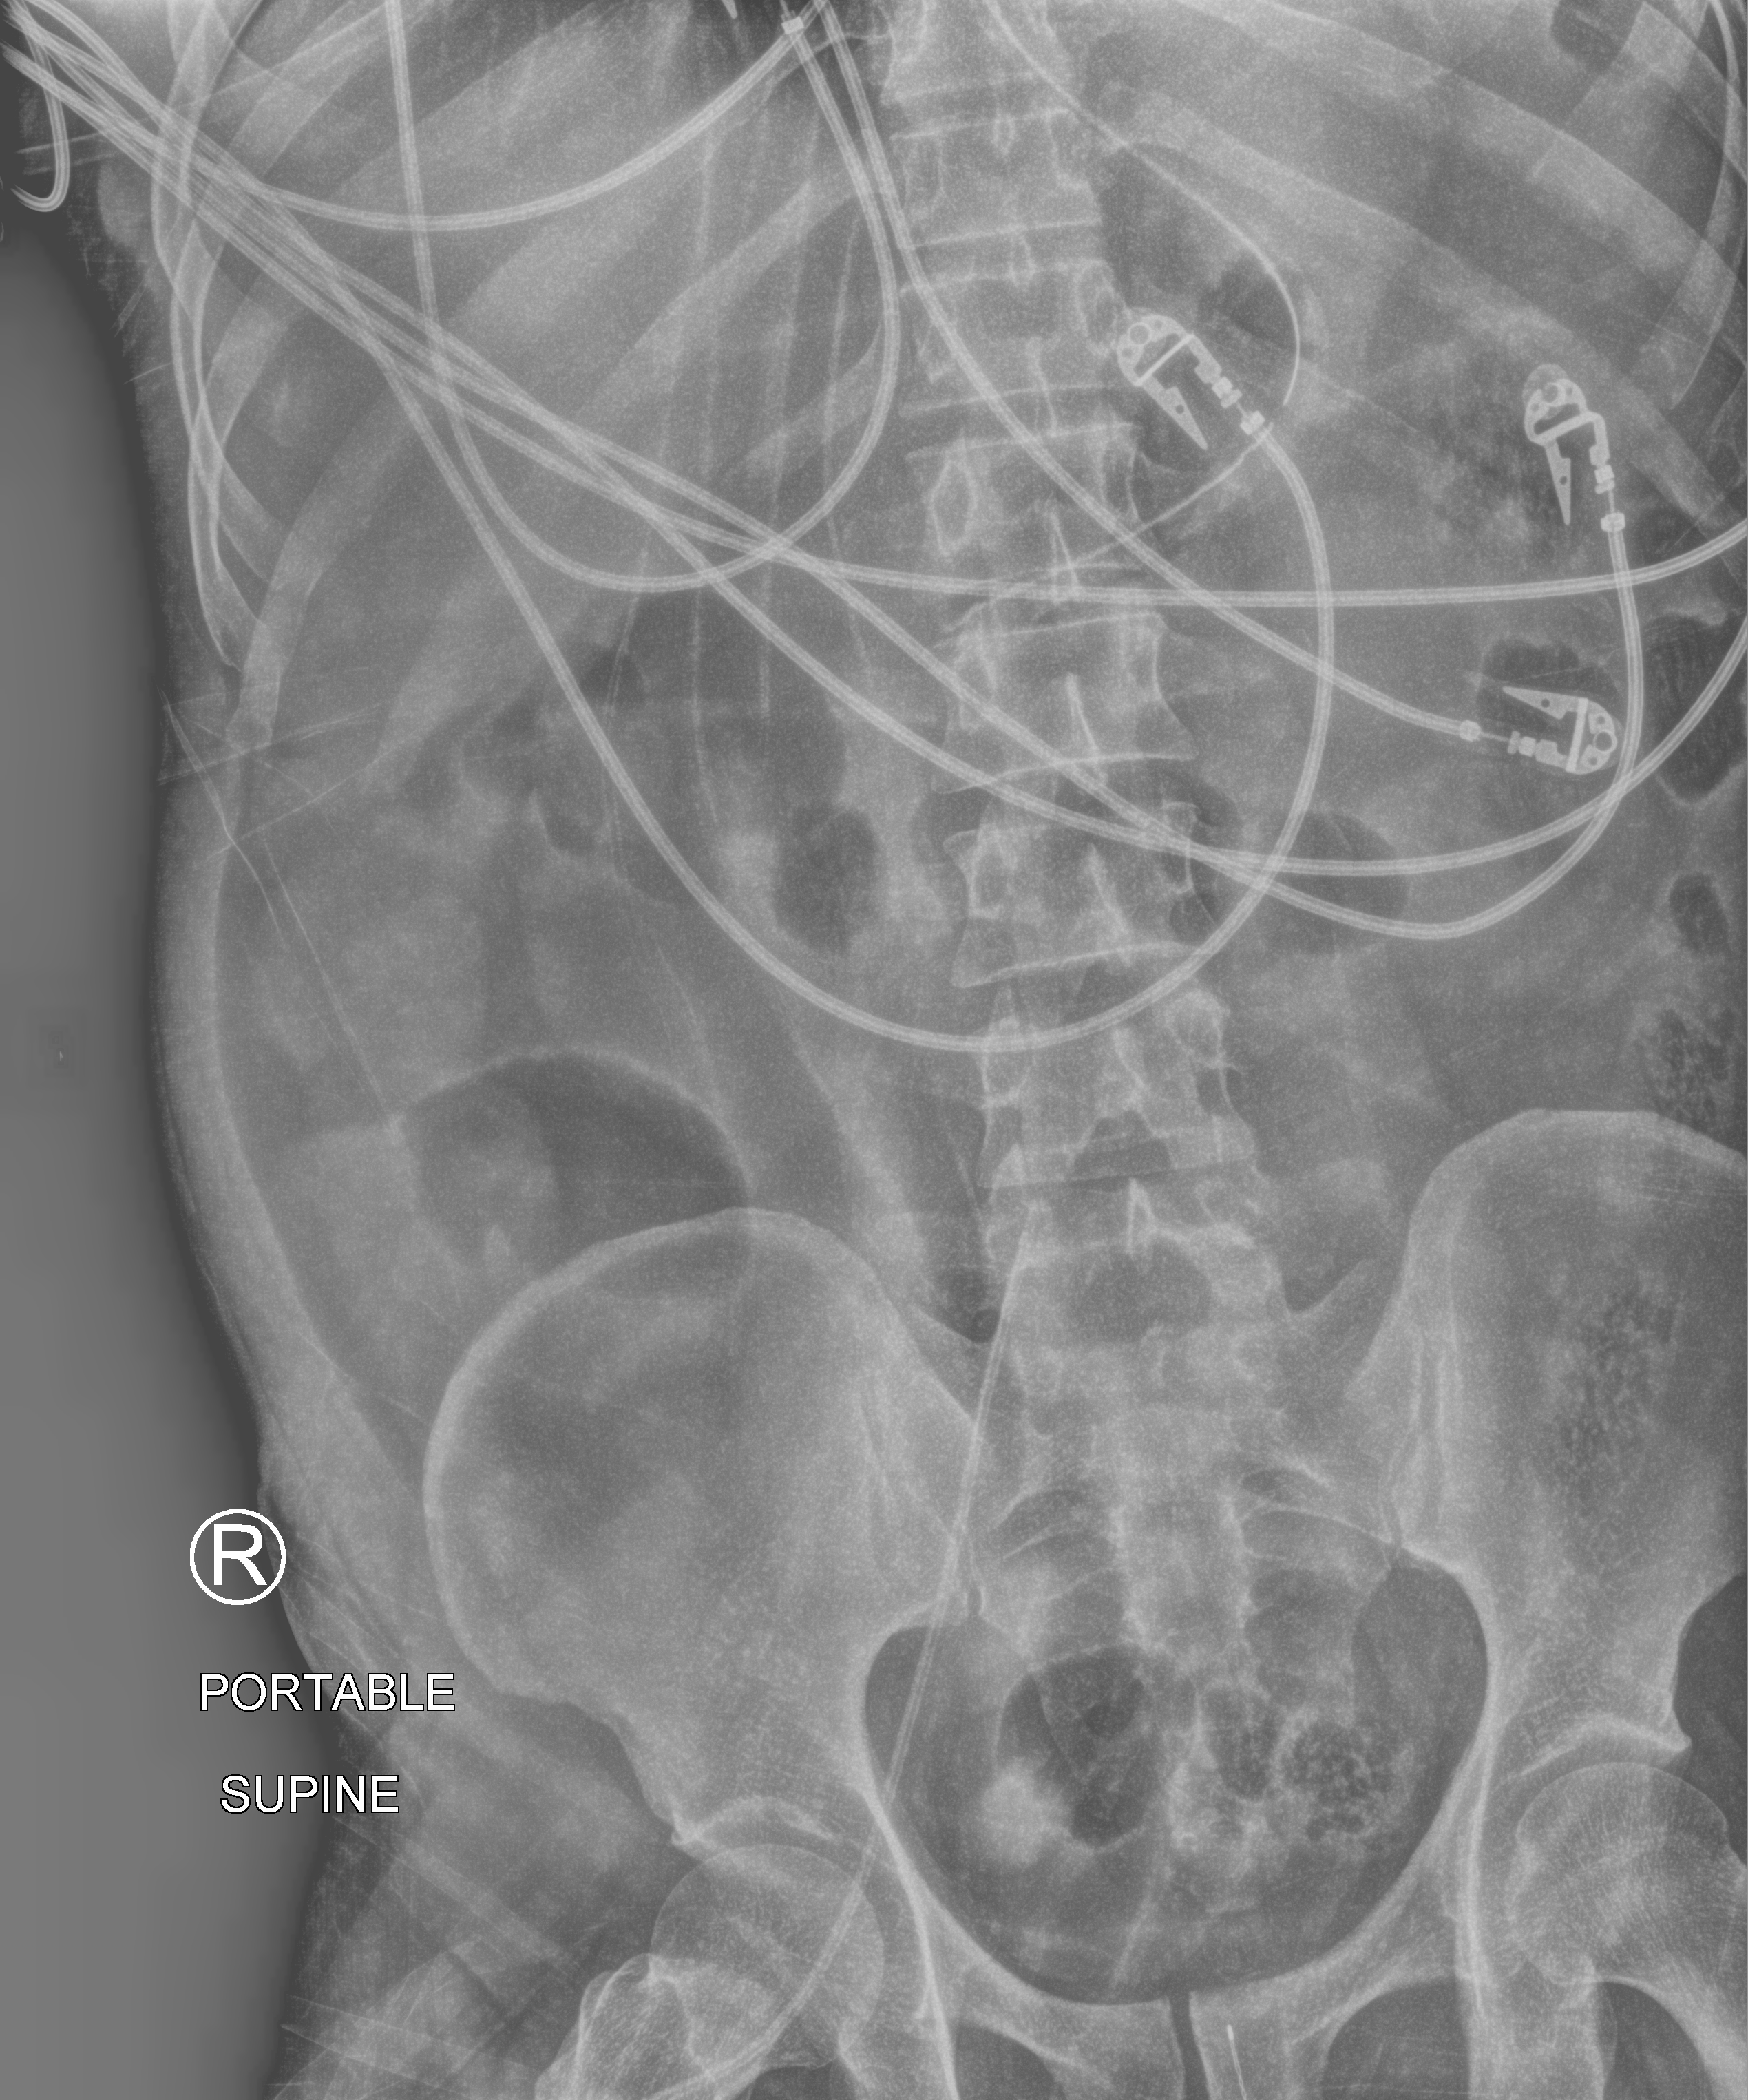
Bedside abdomen radiograph (computed radiography), anteroposterior (AP) projection. Male patient hospitalised with COVID-19, age 18–59 years.
Hospital-stay facts (about this admission, not read from this image; timing relative to this image not recorded):
- admitted to intensive care during this hospital stay: yes
- mechanically ventilated during this hospital stay: yes
- length of hospital stay: 31 days